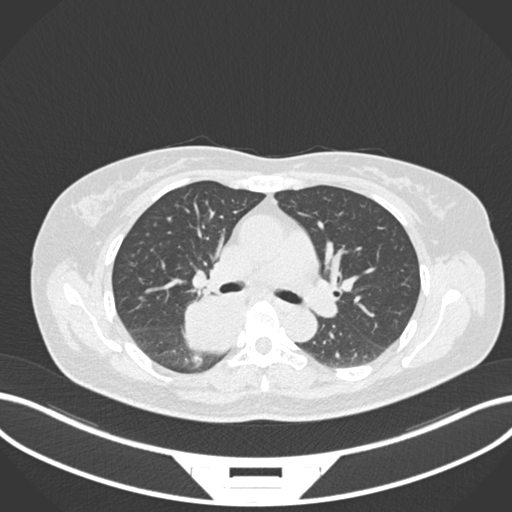
Chest CT, one axial slice. Position 613 of 677 along the scan axis. Reconstruction kernel B30f. 120 kVp. Lung window (W 1500 / L -600 HU). 1 mm slice thickness. 512 × 512 image matrix, field of view 400 × 400 mm. Female patient, age 54 years. Case-level facts recorded for this patient, not image findings: clinical TNM (as recorded): T4 N0 M0.
Outlined on this slice (bounding box drawn by a radiologist):
- lung tumour (recorded histology: adenocarcinoma): bounding box [x1, y1, x2, y2] px = [180, 282, 253, 356]